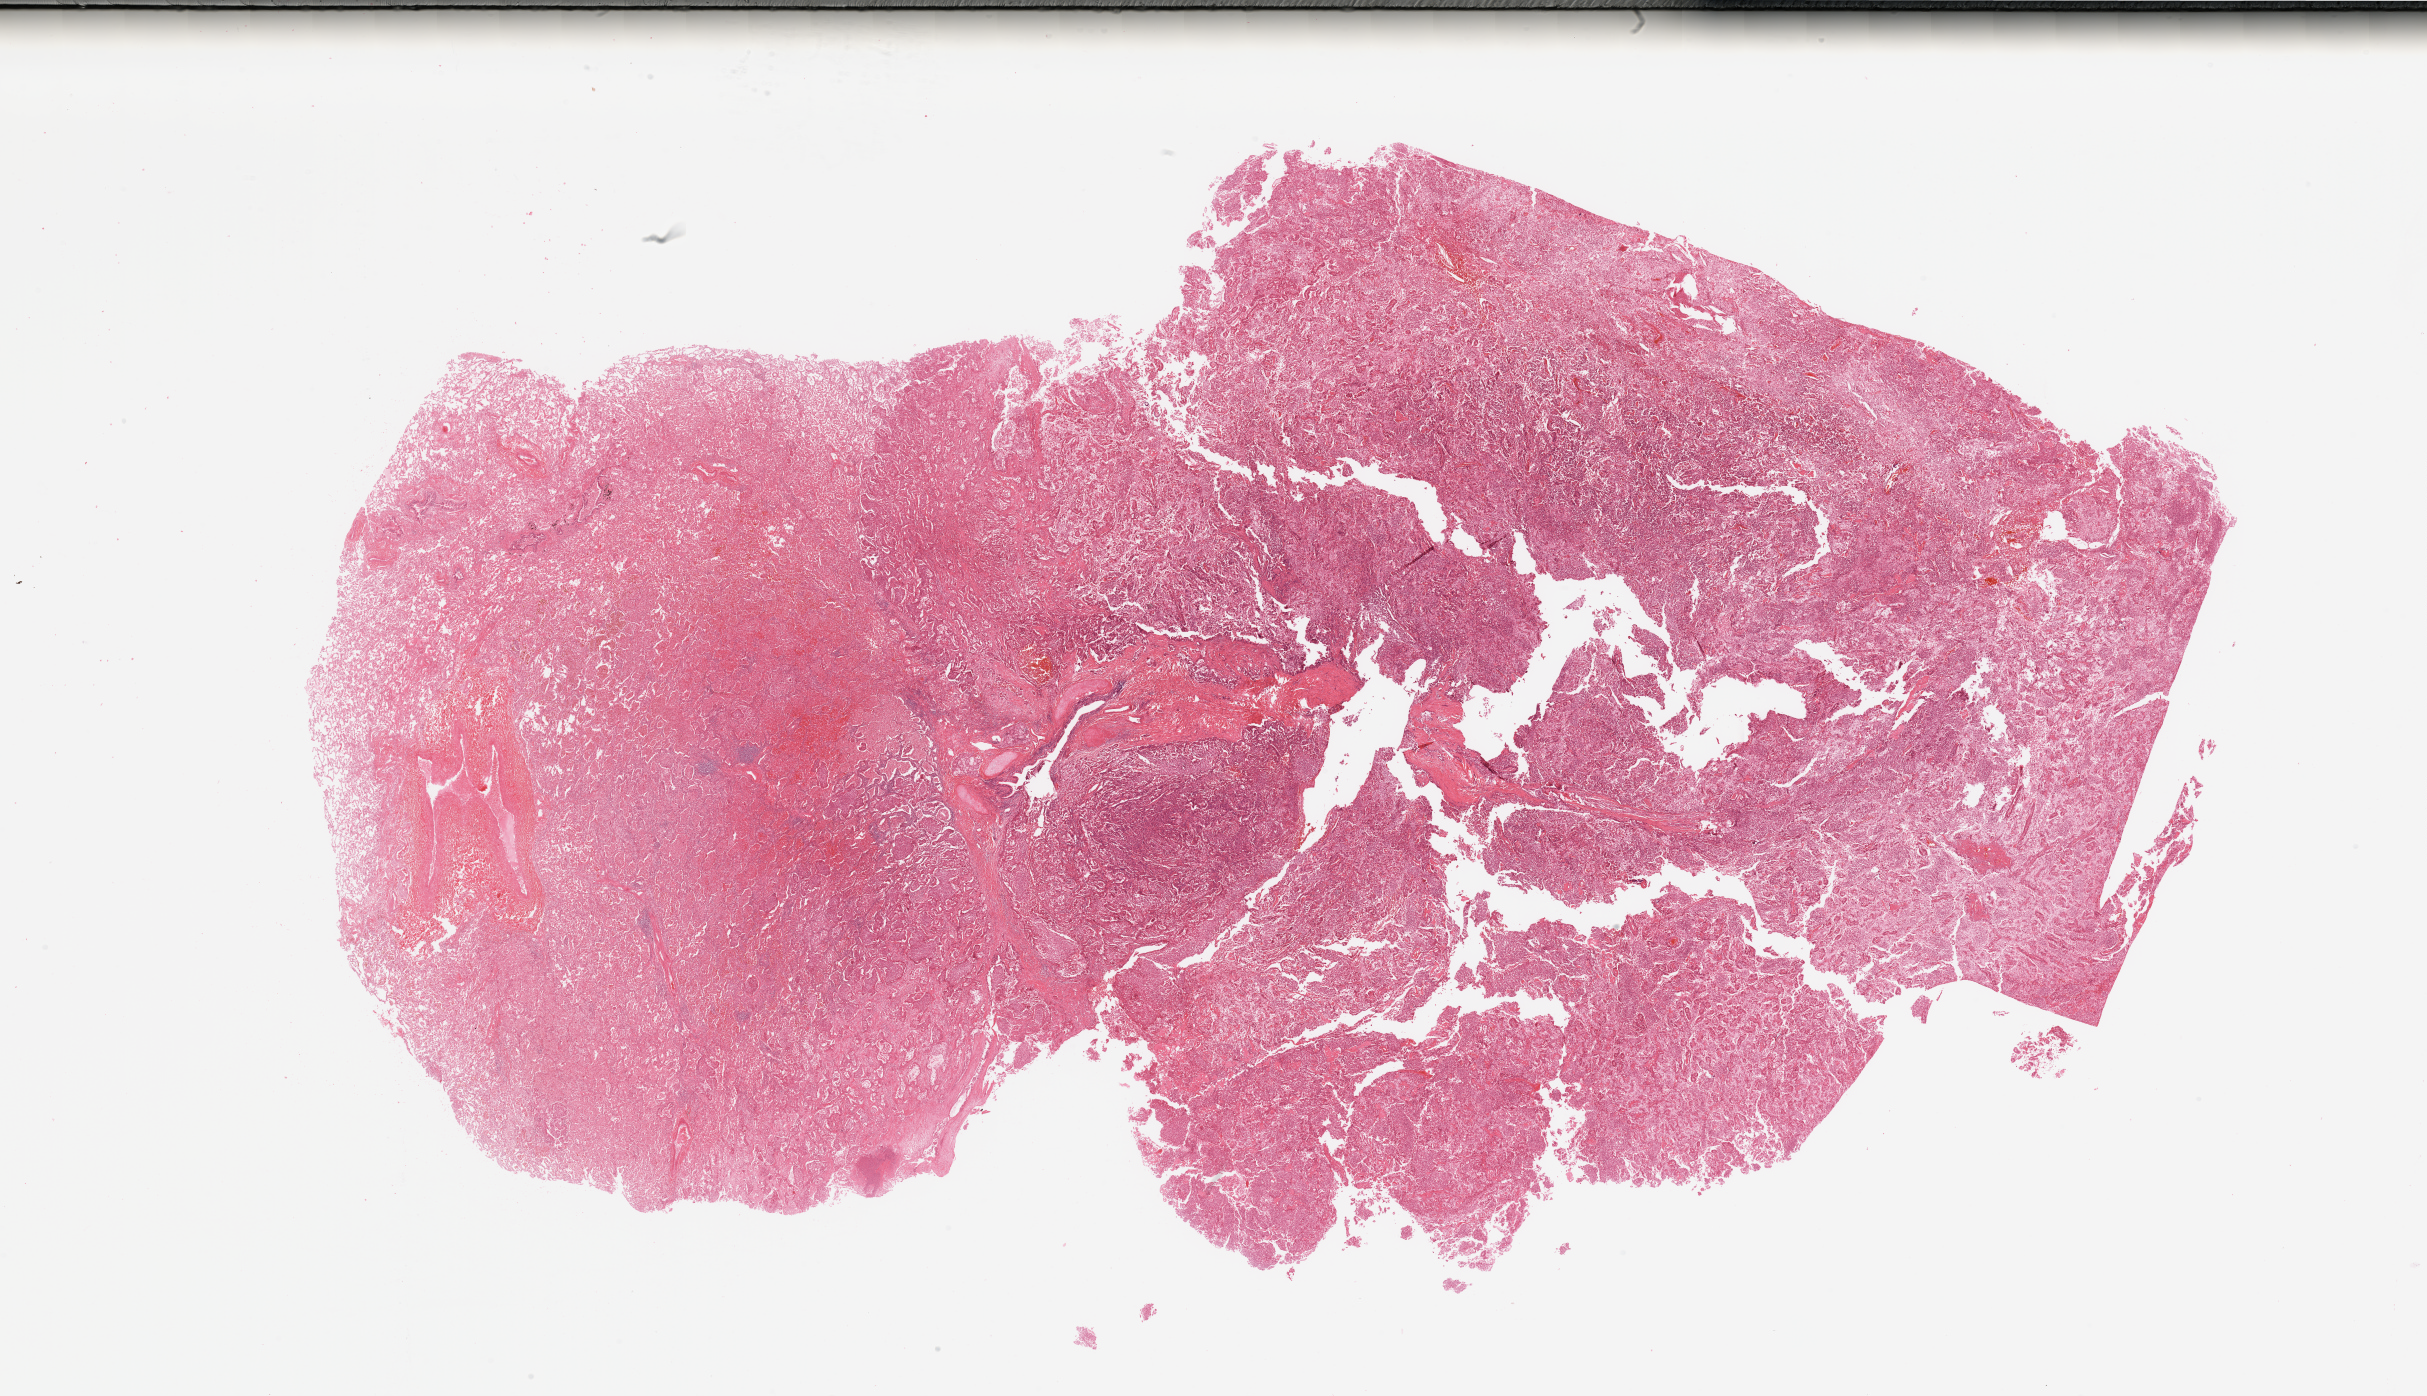
Digitized Hematoxylin and eosin (H&E) stained tissue section (whole slide) — low-resolution overview of the scanned area, about 38.4 x 22.1 mm. Lung, tumour tissue. Patient: female, age 25 years. Histologic grade: G2 (moderately differentiated).
Diagnosis: Adenocarcinoma, NOS.